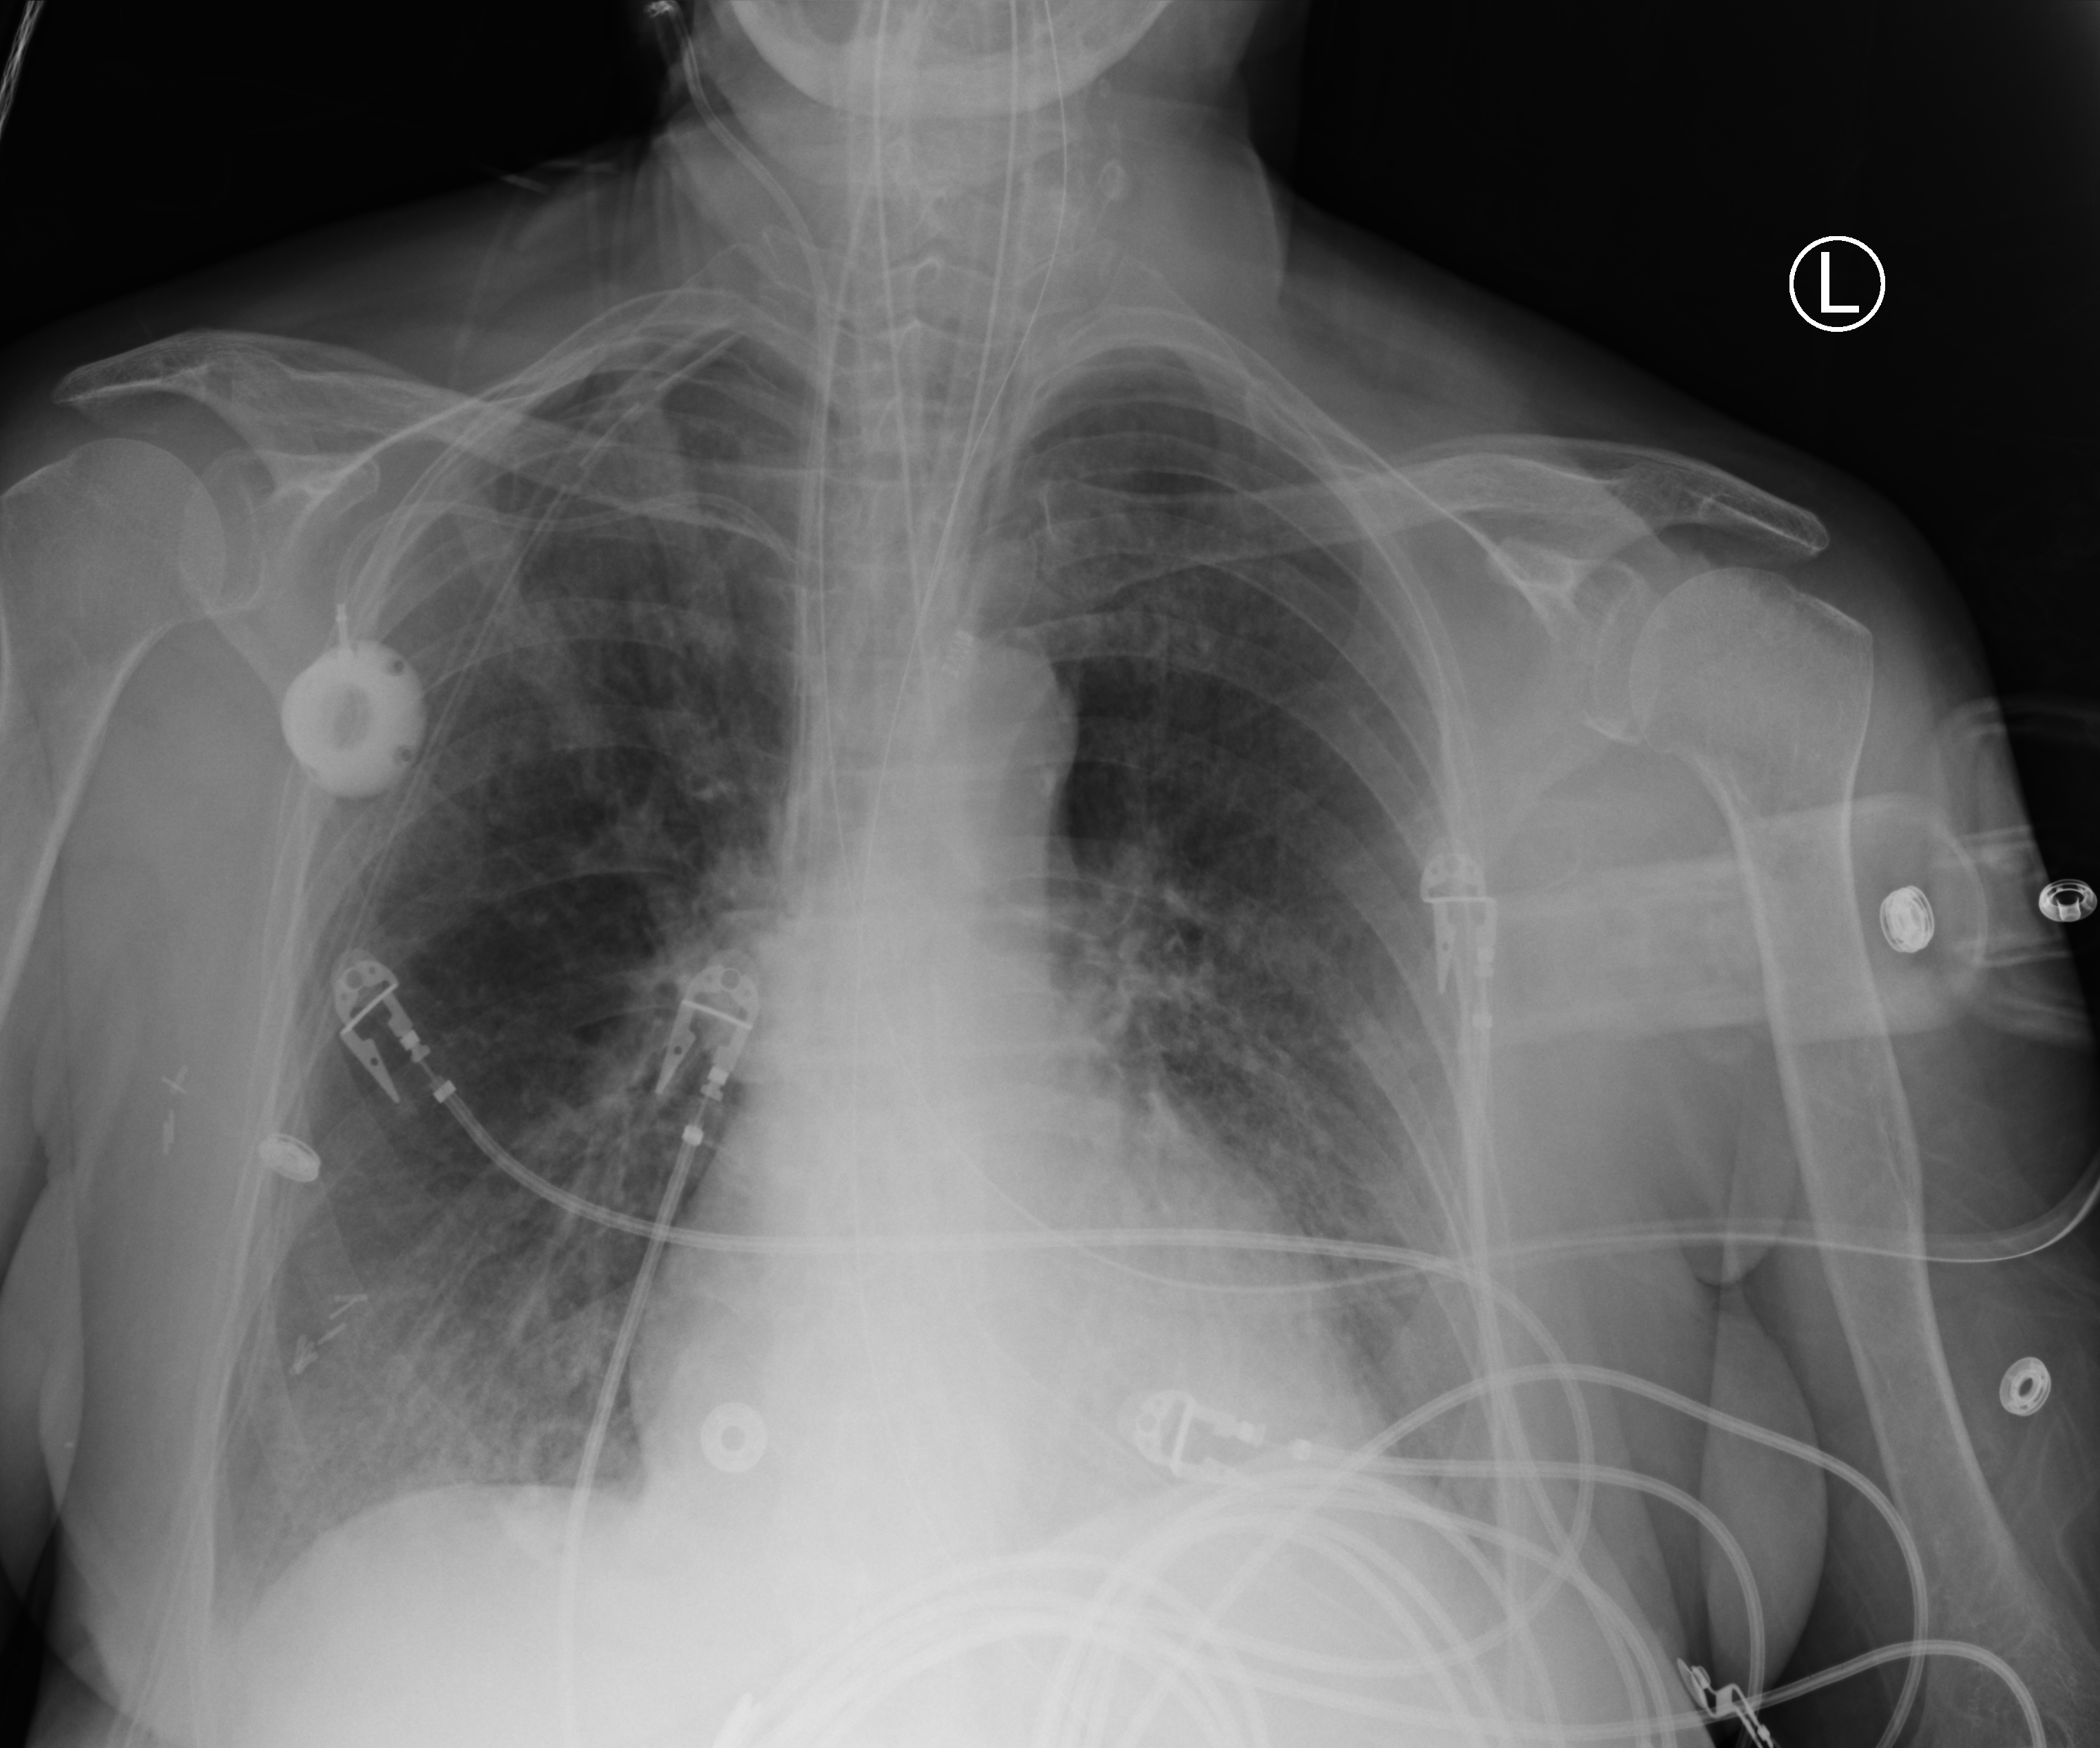
Bedside chest radiograph (computed radiography), anteroposterior (AP) projection. Patient hospitalised with COVID-19; female, aged 60–74 years.
From the hospital-stay record, not from the radiograph (when in the stay this image was taken is not recorded): length of hospital stay: 43 days; COPD (admission record): no; hypertension (admission record): yes.